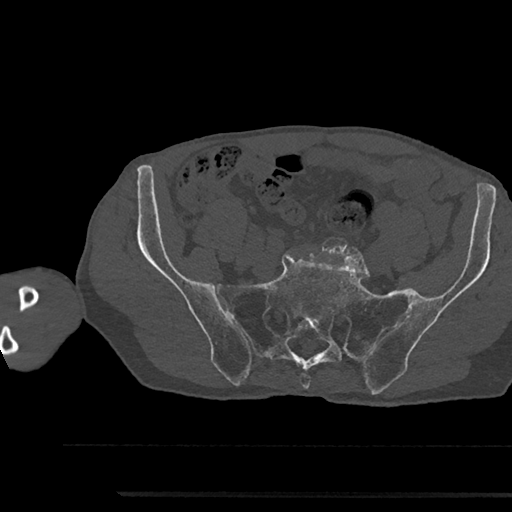
CT including the spine, one axial slice; slice 271 of 797 in the series (ordered by position); 120 kVp; bone window (W 1800 / L 400 HU); 0.5 mm slice thickness; 512 × 512 image matrix. Patient: male, 79 years. Case-level facts recorded for this patient, not image findings: primary cancer: prostate.
Outlined on this slice (semi-automatically segmented with operator editing):
- L5 vertebra: bounding box [x1, y1, x2, y2] px = [306, 243, 310, 246]